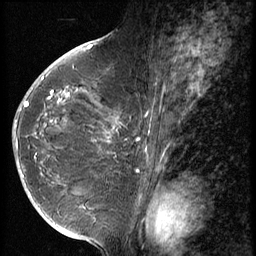
Breast MRI (dynamic contrast-enhanced), one sagittal slice. 3 images stored at this slice position (order not interpretable as contrast timing). 1.5 T. TE 4.2 ms, TR 9 ms. 2.5 mm slice thickness. 256 × 256 image matrix, field of view 180 × 180 mm. Patient: female, 49 years. Case-level facts recorded for this patient, not image findings: setting: breast cancer imaged before/during neoadjuvant chemotherapy; receptor status: HER2-positive.
Outlined on this slice (semi-automatic segmentation, software-assisted and operator-edited):
- analysis volume of interest (the breast-tissue region the enhancement analysis was run in; not a lesion): bounding box <13,79,117,203> (left, top, right, bottom; pixels)
- tumour enhancement mask (voxels above the 140 % enhancement threshold inside the analysis volume of interest): <14,125,110,179>